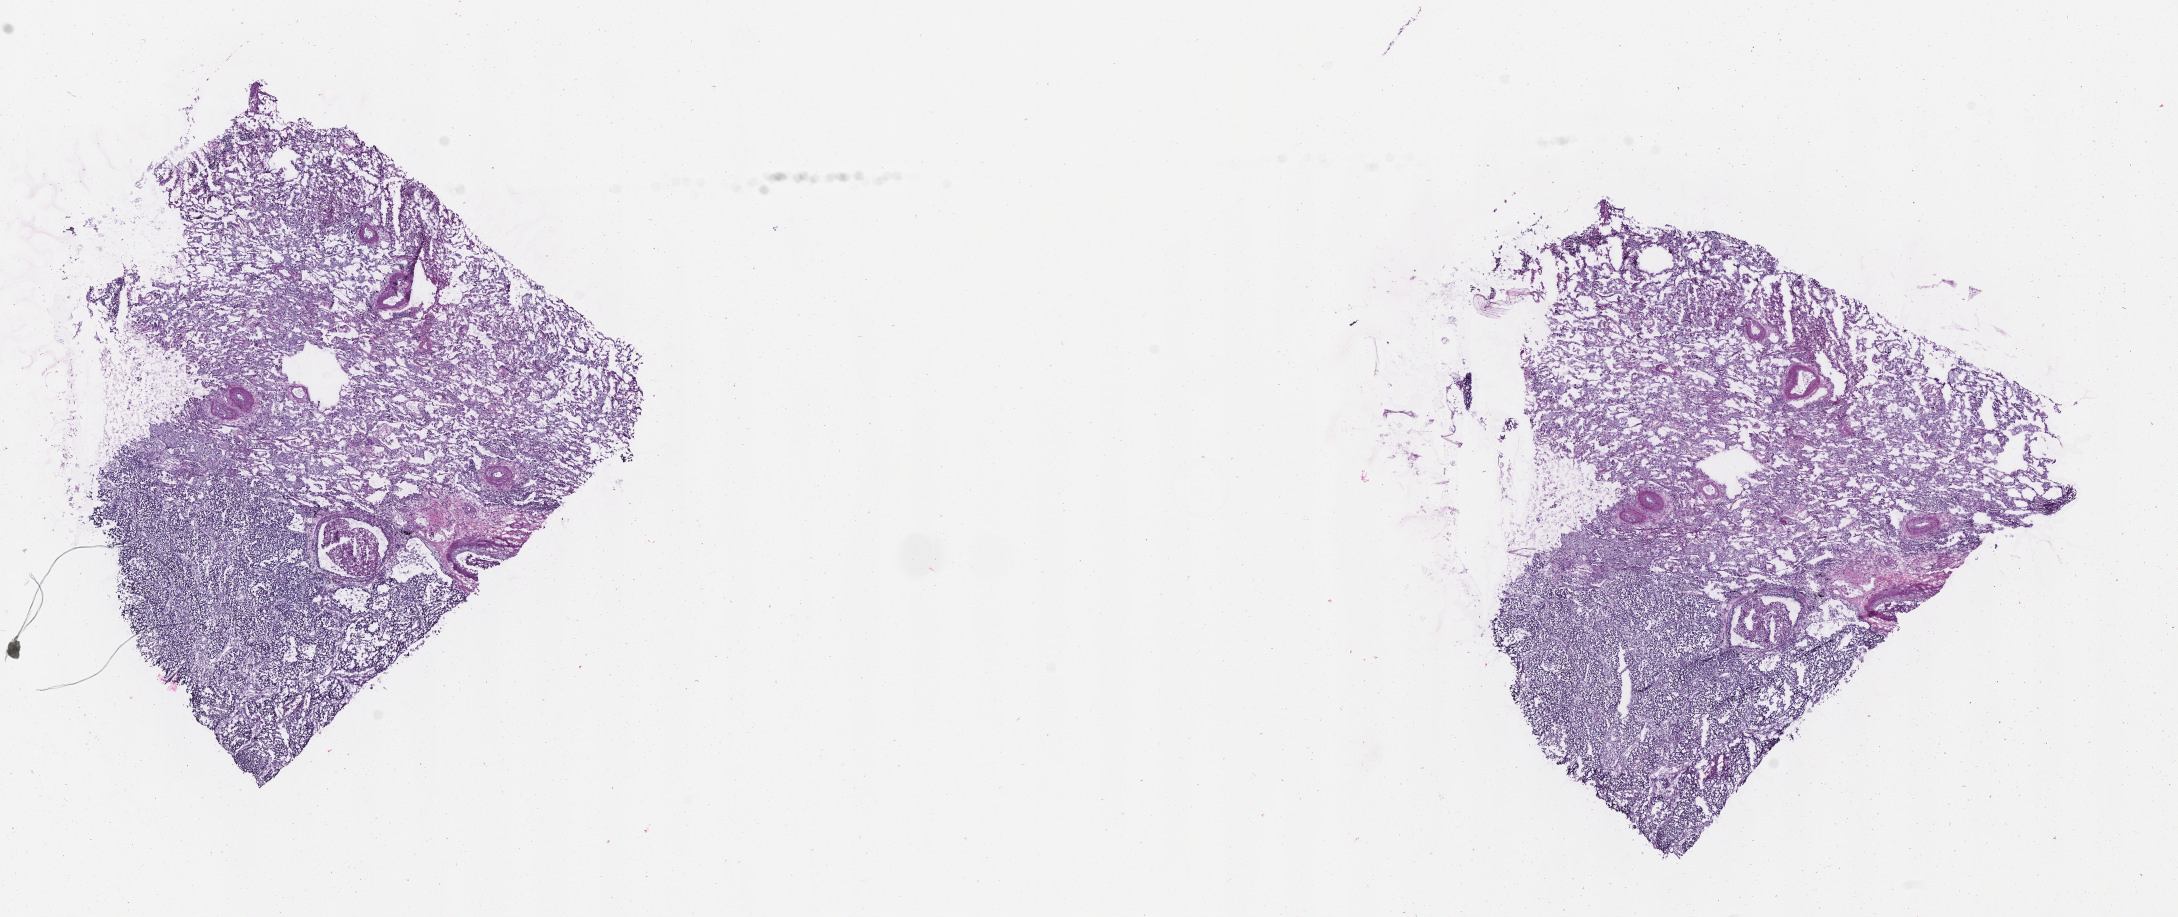
Whole-slide image, hematoxylin and eosin (H&E) stain — a low-resolution overview of the entire scanned area, about 17.6 x 7.4 mm; frozen section (tissue freezing medium); primary tumor; site: upper lobe of right lung. Patient male; 67 years old. Pathologist review of this section (percent, as recorded): tumor cells 70%, tumor nuclei 70%, stromal cells 20%, necrosis 5%, normal cells 5%. Inflammatory infiltration, as recorded: lymphocyte infiltration 4%, monocyte infiltration 4%, neutrophil infiltration 4%.
Section: top of the tissue portion. AJCC pathologic stage: Stage IIB. Diagnosis: Adenocarcinoma, NOS.